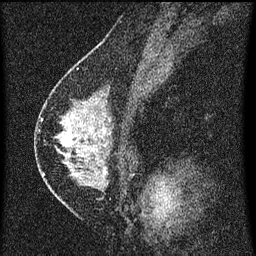
Breast MRI (dynamic contrast-enhanced), one sagittal slice; slice 33 of 60 in the series (ordered by position); dynamic contrast-enhanced series, image 2 of 3 at this slice position (ordered by acquisition); 1.5 T; TE 4.2 ms, TR 8 ms; 2 mm slice thickness; 256 × 256 image matrix, field of view 180 × 180 mm. Patient: female, 47 years.
Structures marked on this image (semi-automatic segmentation, software-assisted and operator-edited):
- analysis volume of interest (the breast-tissue region the enhancement analysis was run in; not a lesion): box from (x=42, y=92) to (x=134, y=199) px
- tumour enhancement mask (voxels above the 70 % enhancement threshold inside the analysis volume of interest): (x=43, y=124)–(x=106, y=177)